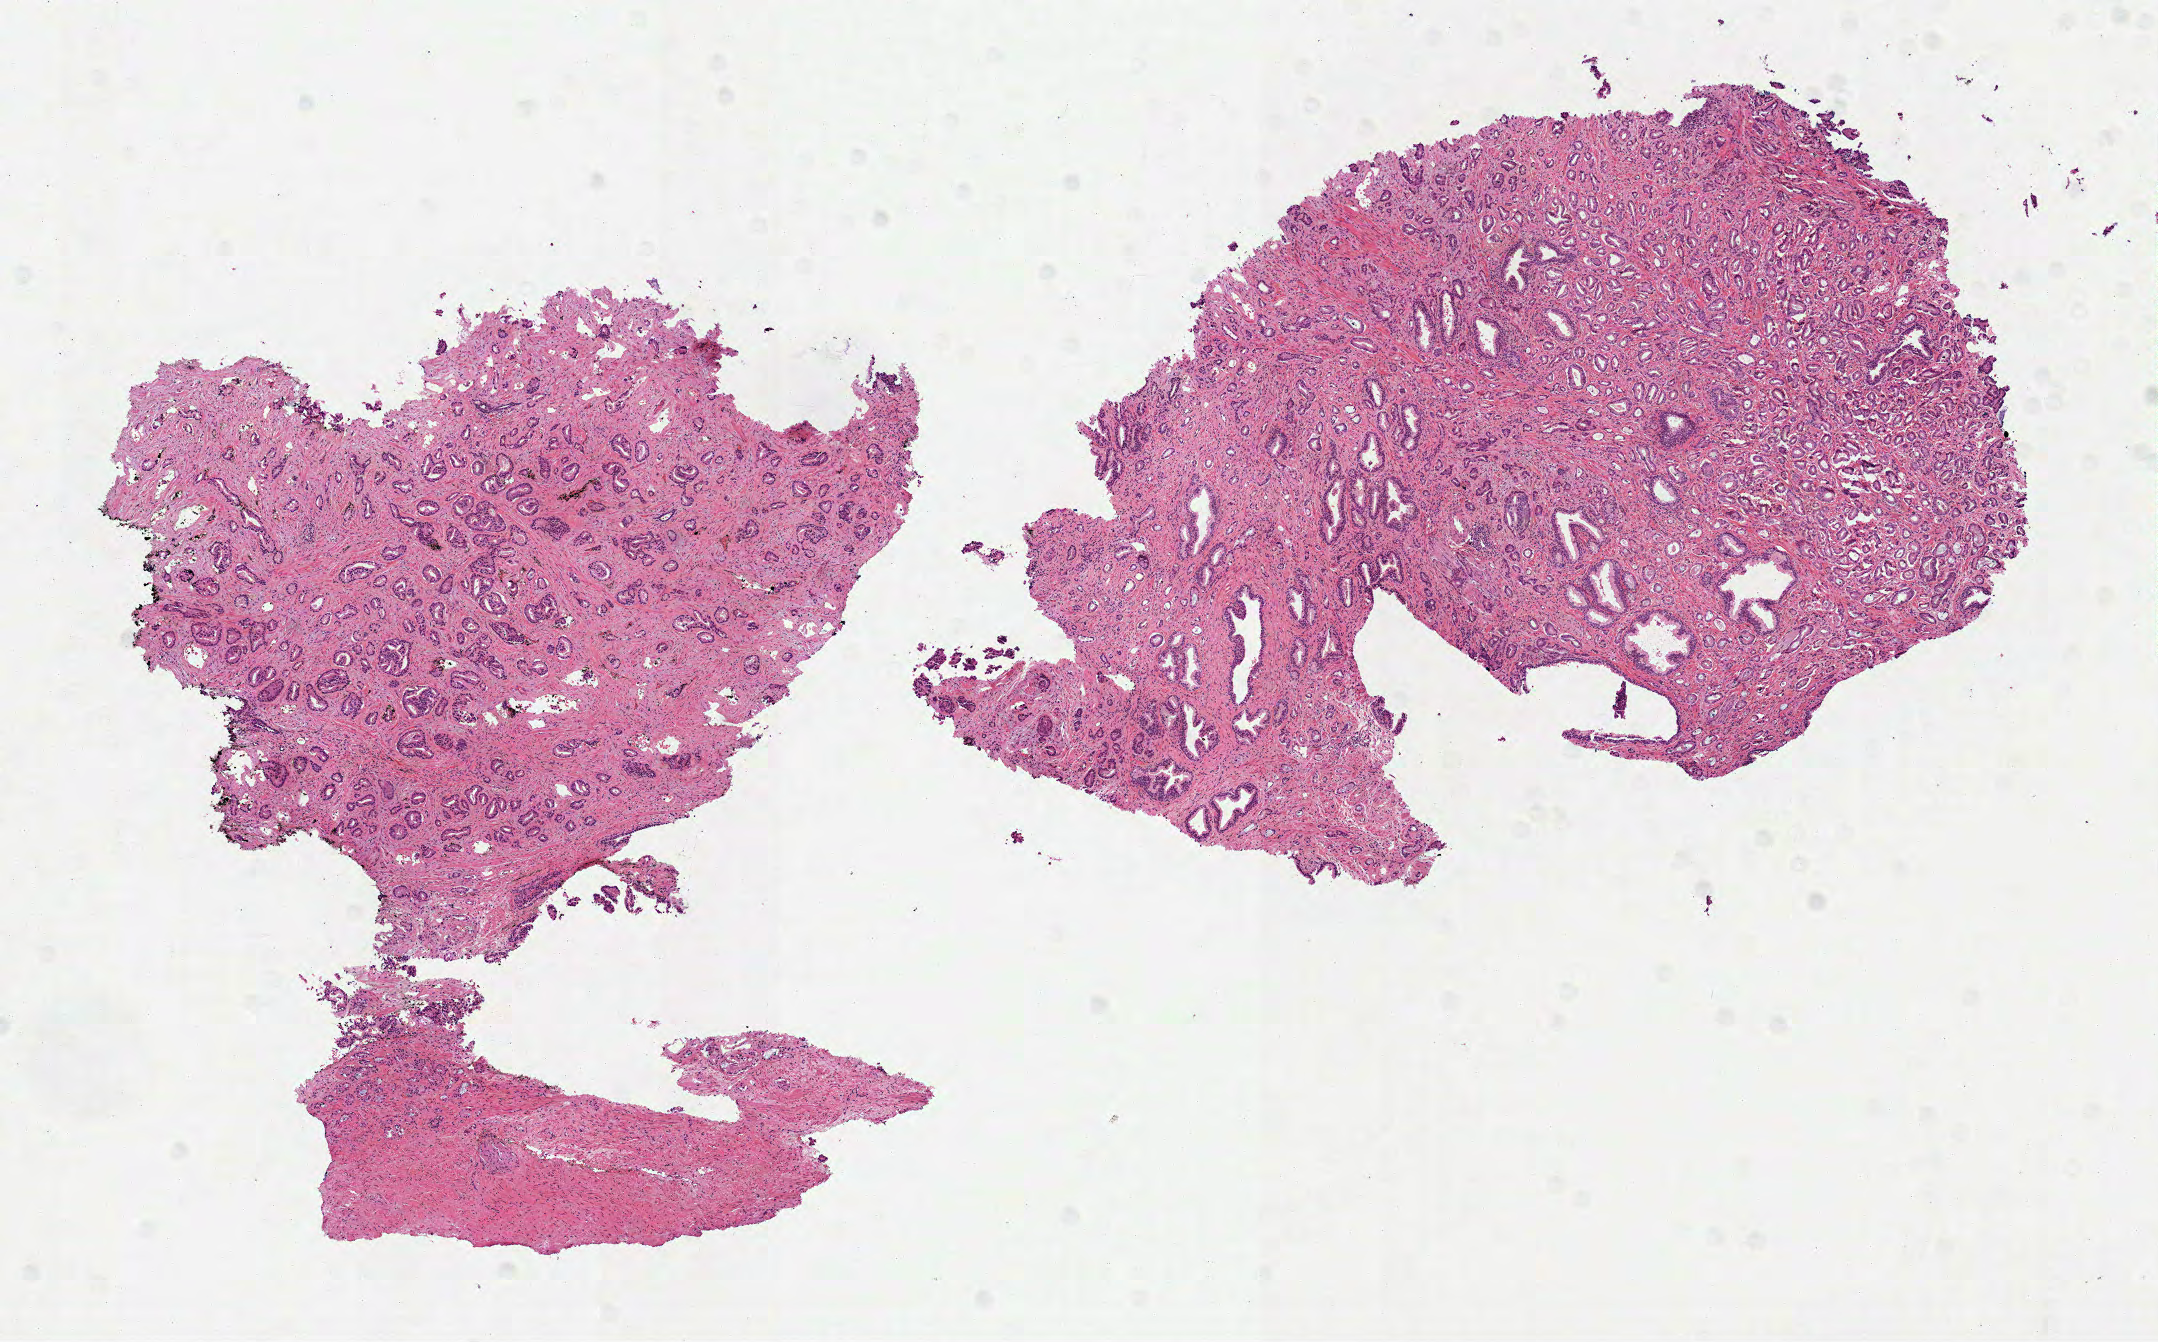
Whole-slide histology image, H&E-stained, low-resolution overview of the scanned area, about 8.7 x 5.4 mm (acquisition: 40x scan); formalin-fixed paraffin-embedded (FFPE) diagnostic section; sample: primary tumour, prostate. Male patient; age at initial diagnosis 43 years. Gleason score: 7 (3+4).
Laterality: bilateral. Diagnosis: Acinar cell carcinoma.